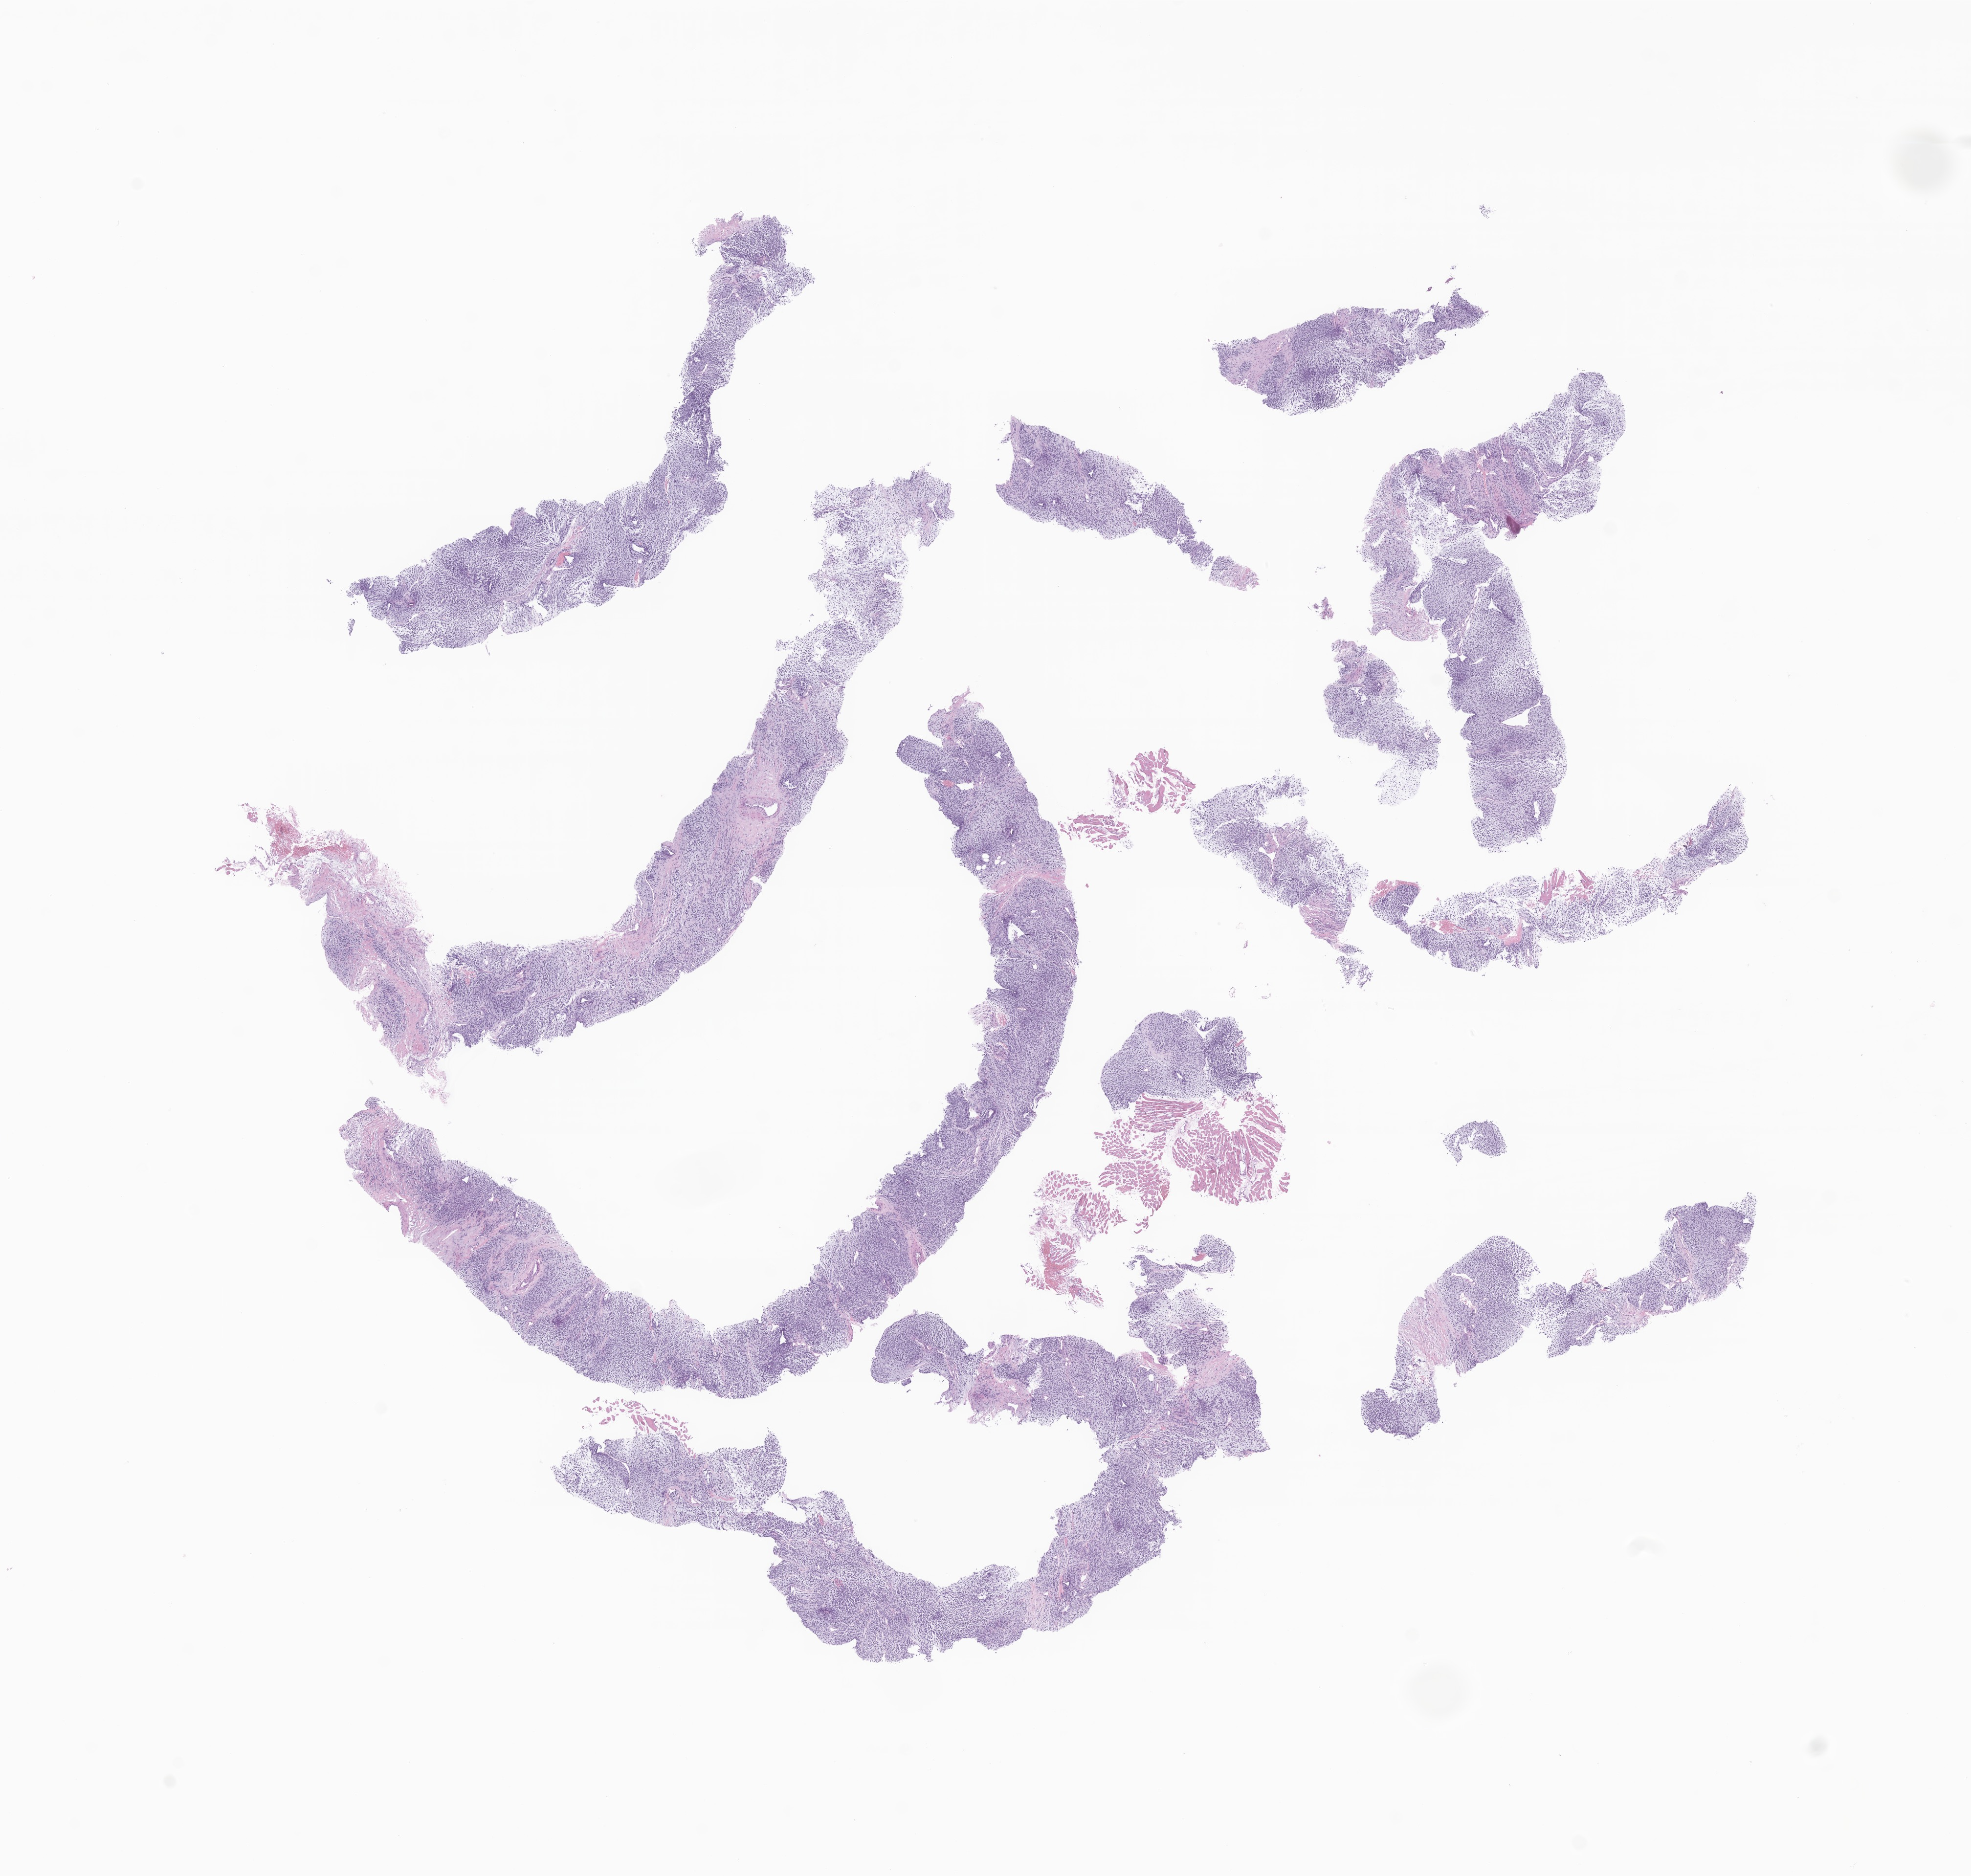
Digitized hematoxylin and eosin (H&E)-stained section of tumor tissue from the soft tissues of head and neck, low-resolution overview of the scanned area, about 17.0 x 16.2 mm, formalin-fixed paraffin-embedded section. Patient: female, age 145 months (12 years 1 month).
• diagnosis (ICD-O-3 morphology term): Embryonal rhabdomyosarcoma, NOS